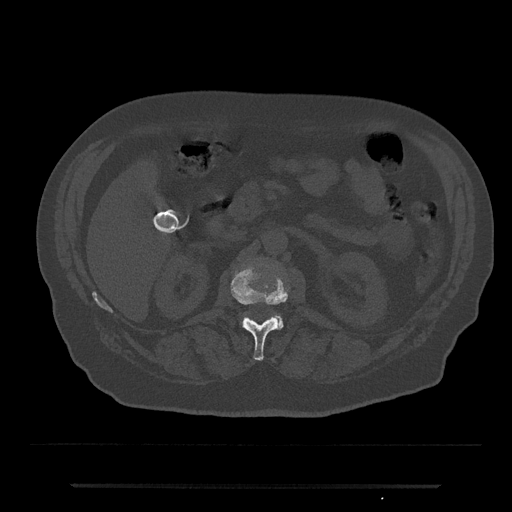
CT including the spine, one axial slice. Bone window (W 1800 / L 400 HU). 512 × 512 image matrix, field of view 434 × 434 mm. Patient: male, 80 years. From the clinical record (not read from this slice): primary cancer: prostate; vertebrae with lytic lesions (as recorded): L1, T11.
Outlined on this slice (semi-automatic segmentation, software-assisted and operator-edited):
- L1 vertebra: box from (x=231, y=267) to (x=287, y=361) px
- L2 vertebra: (x=274, y=314)–(x=284, y=329)